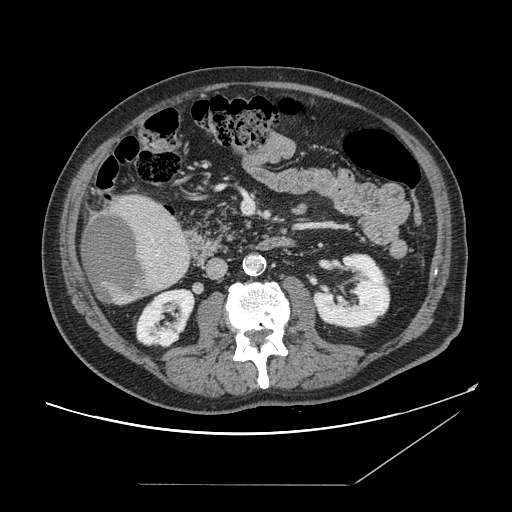
Contrast-enhanced abdominal CT, one axial slice; position 53 of 166 along the scan axis; 120 kVp; intravenous contrast given; soft-tissue window (W 400 / L 40 HU); 512 × 512 image matrix, field of view 416 × 416 mm. Male patient, age 80 years. From the clinical record (not read from this slice): diagnosis: colorectal cancer liver metastases, imaged before liver resection; multiple liver metastases: no; largest metastasis: 2.2 cm; disease in both lobes: no.
Structures marked on this image (manually delineated by an expert):
- liver: bounding box (x1, y1, x2, y2) in pixels: (81, 194, 190, 304)
- liver metastasis: (84, 212, 148, 301)